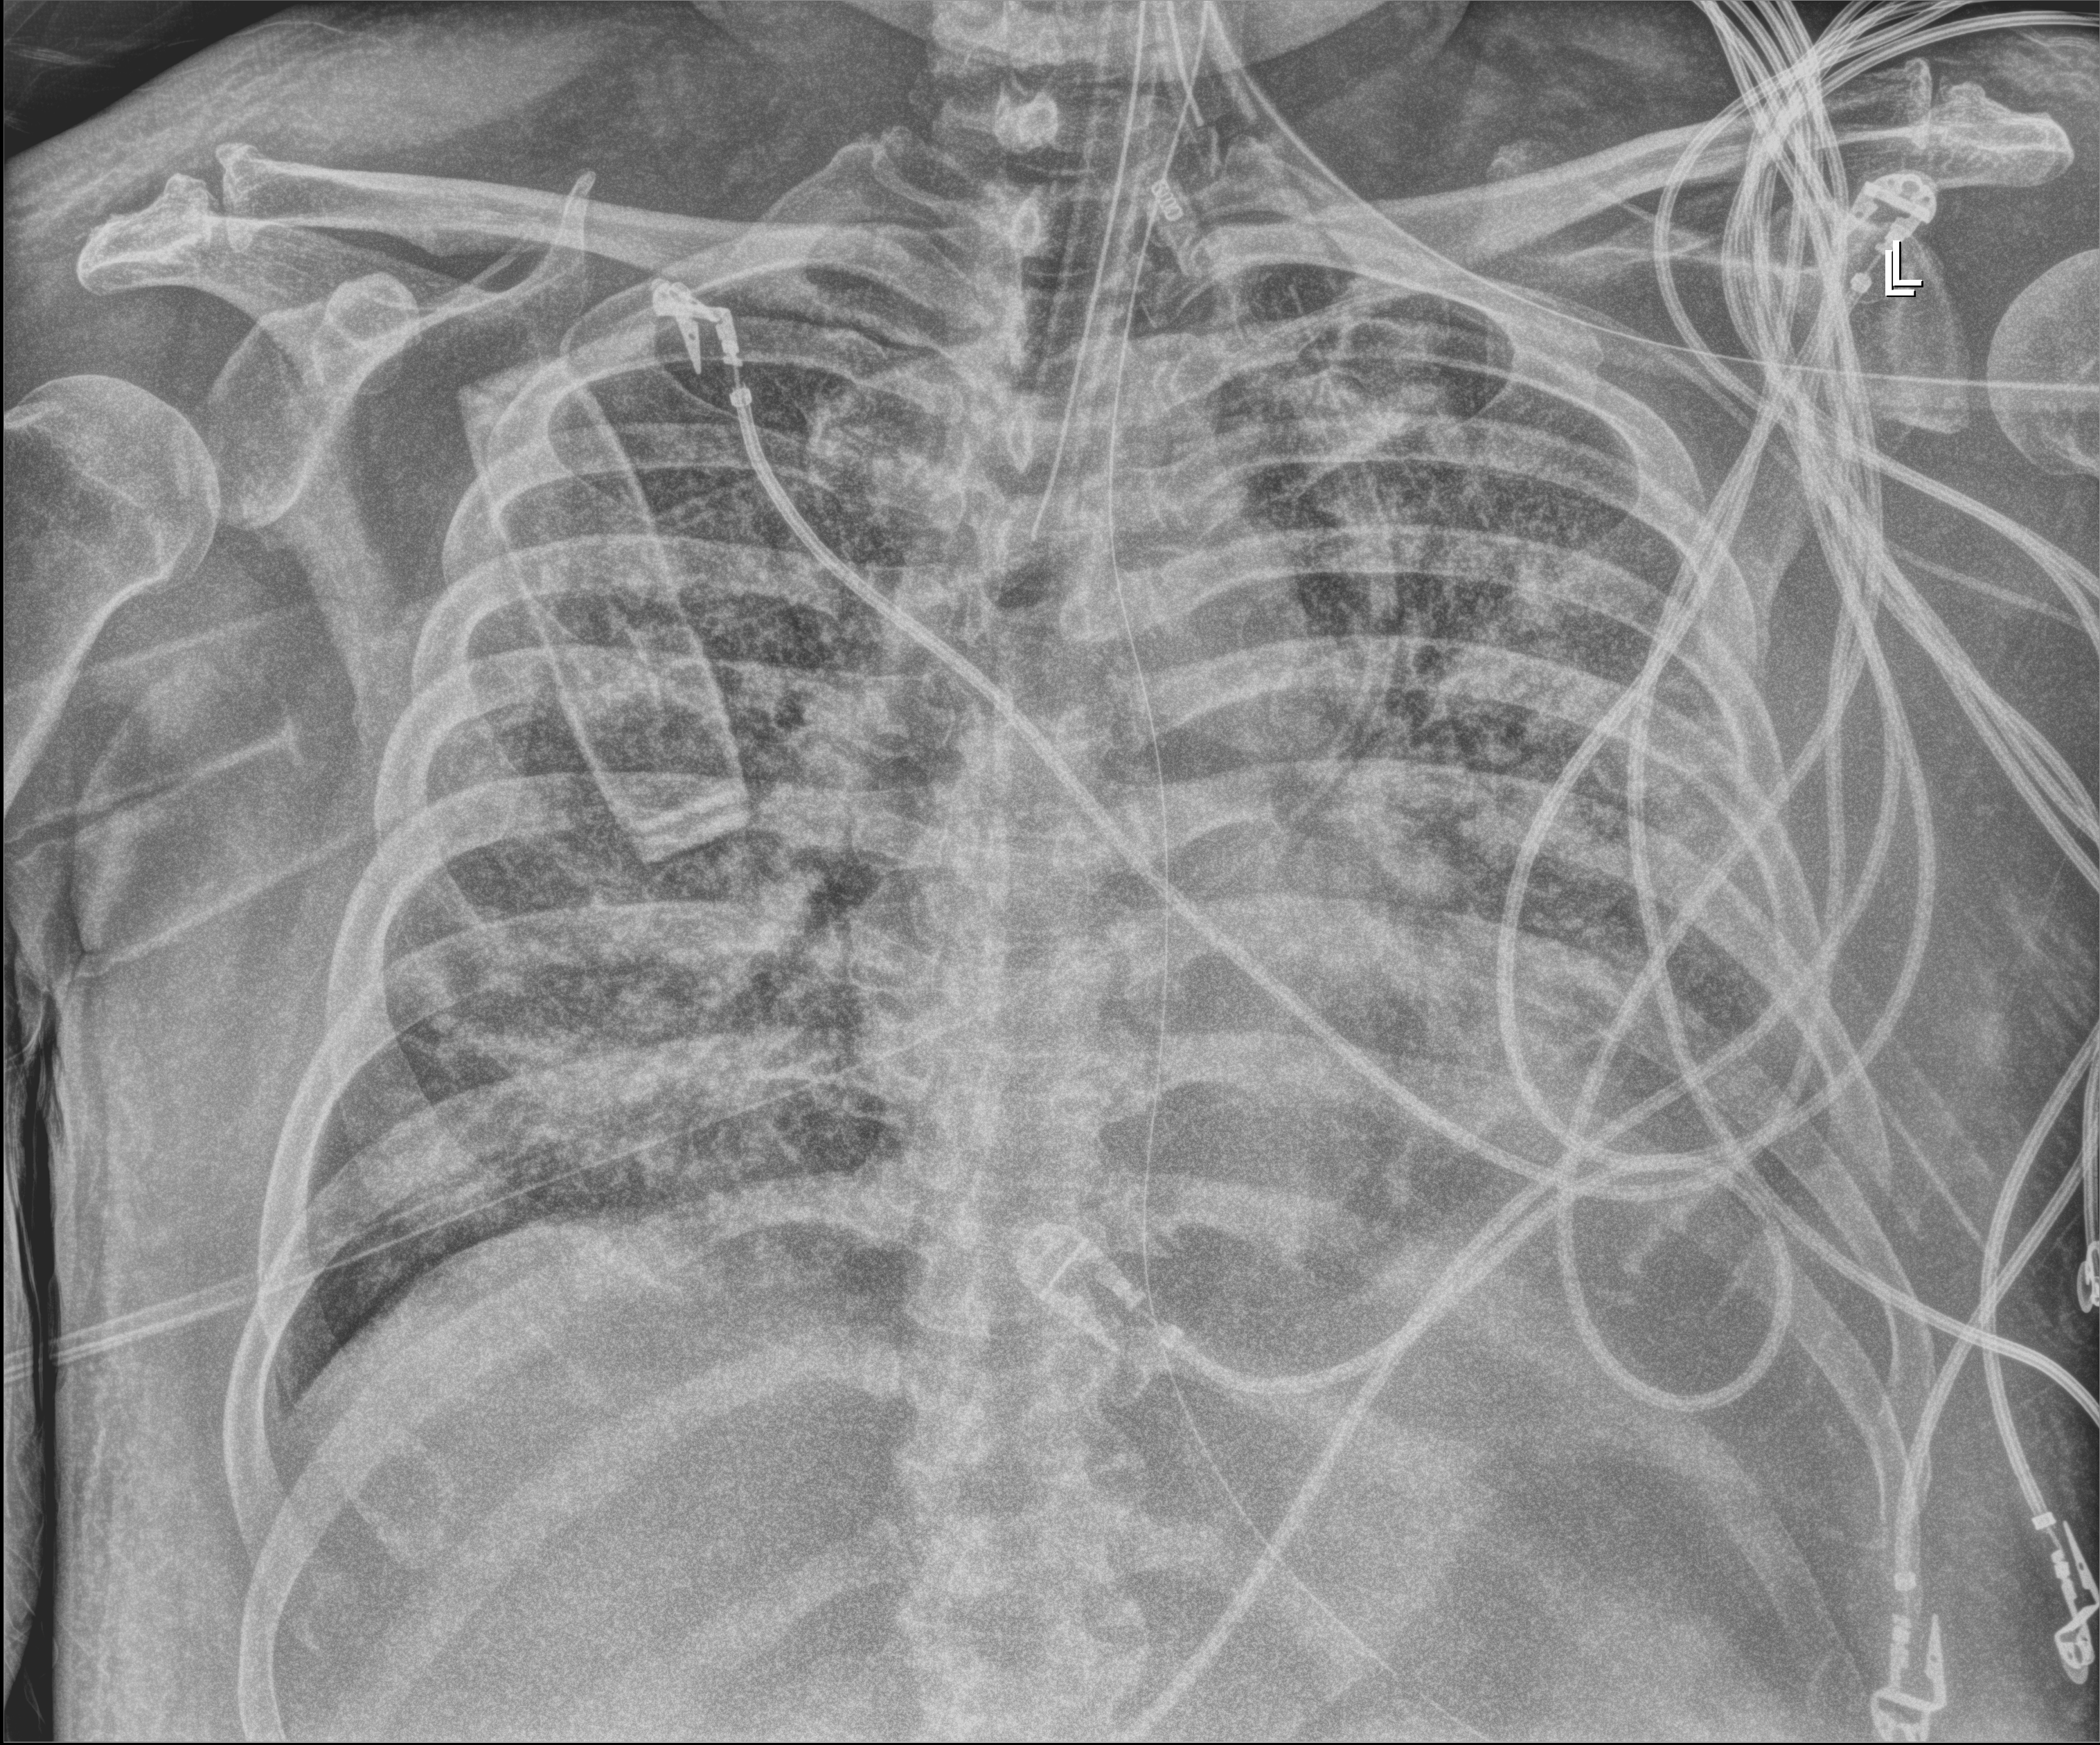
Chest X-ray (portable). Male patient hospitalised with COVID-19, age 60–74 years.
From the hospital-stay record, not from the radiograph (when in the stay this image was taken is not recorded): admitted to intensive care during this hospital stay: yes; mechanically ventilated during this hospital stay: yes.